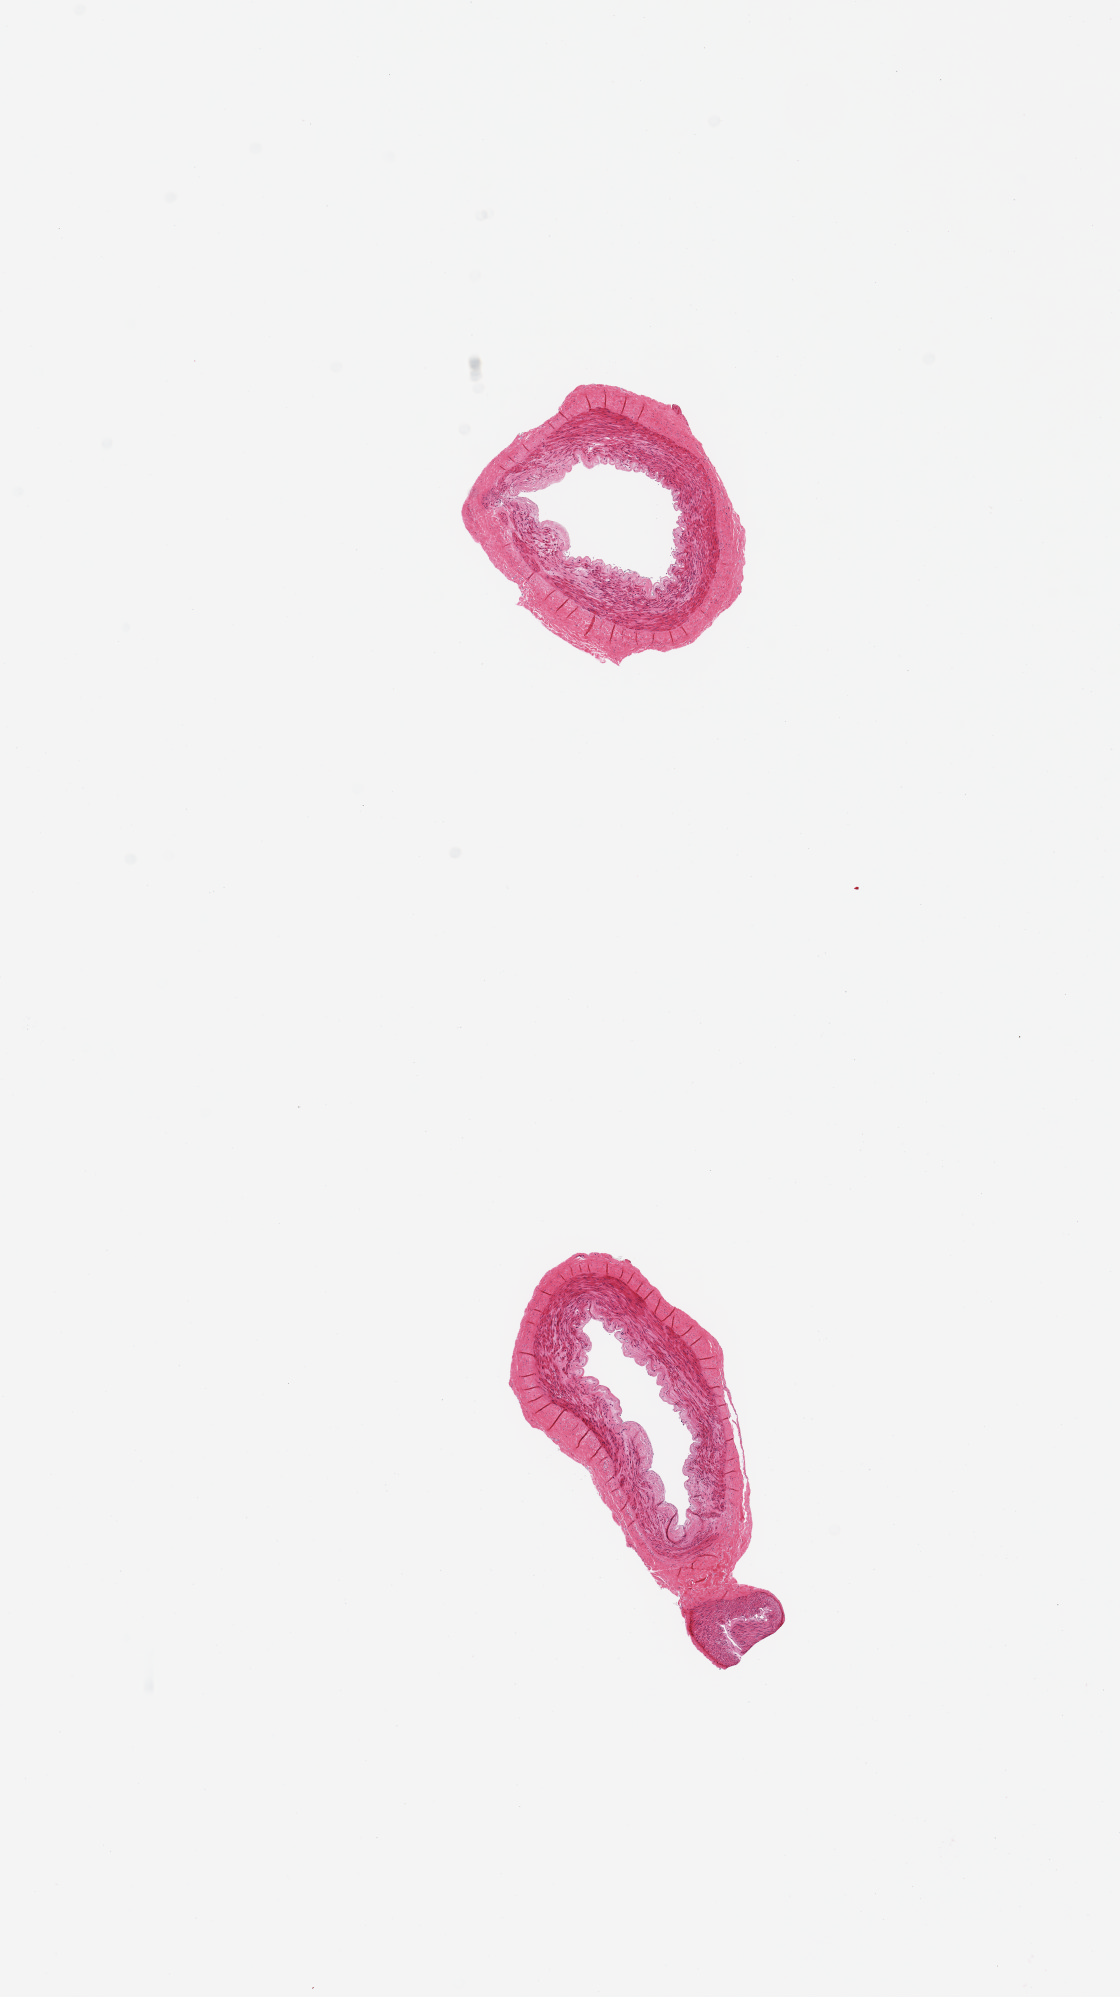
Digitized H&E-stained section, brightfield — low-resolution overview of the scanned area, about 8.9 x 15.8 mm. PAXgene-fixed paraffin-embedded (PFPE) section. Section of tibial artery (target tissue). Donor tissue sample. Donor sex: female.
- review note (as recorded): 2 pieces, no adherent fat or significant atherosis